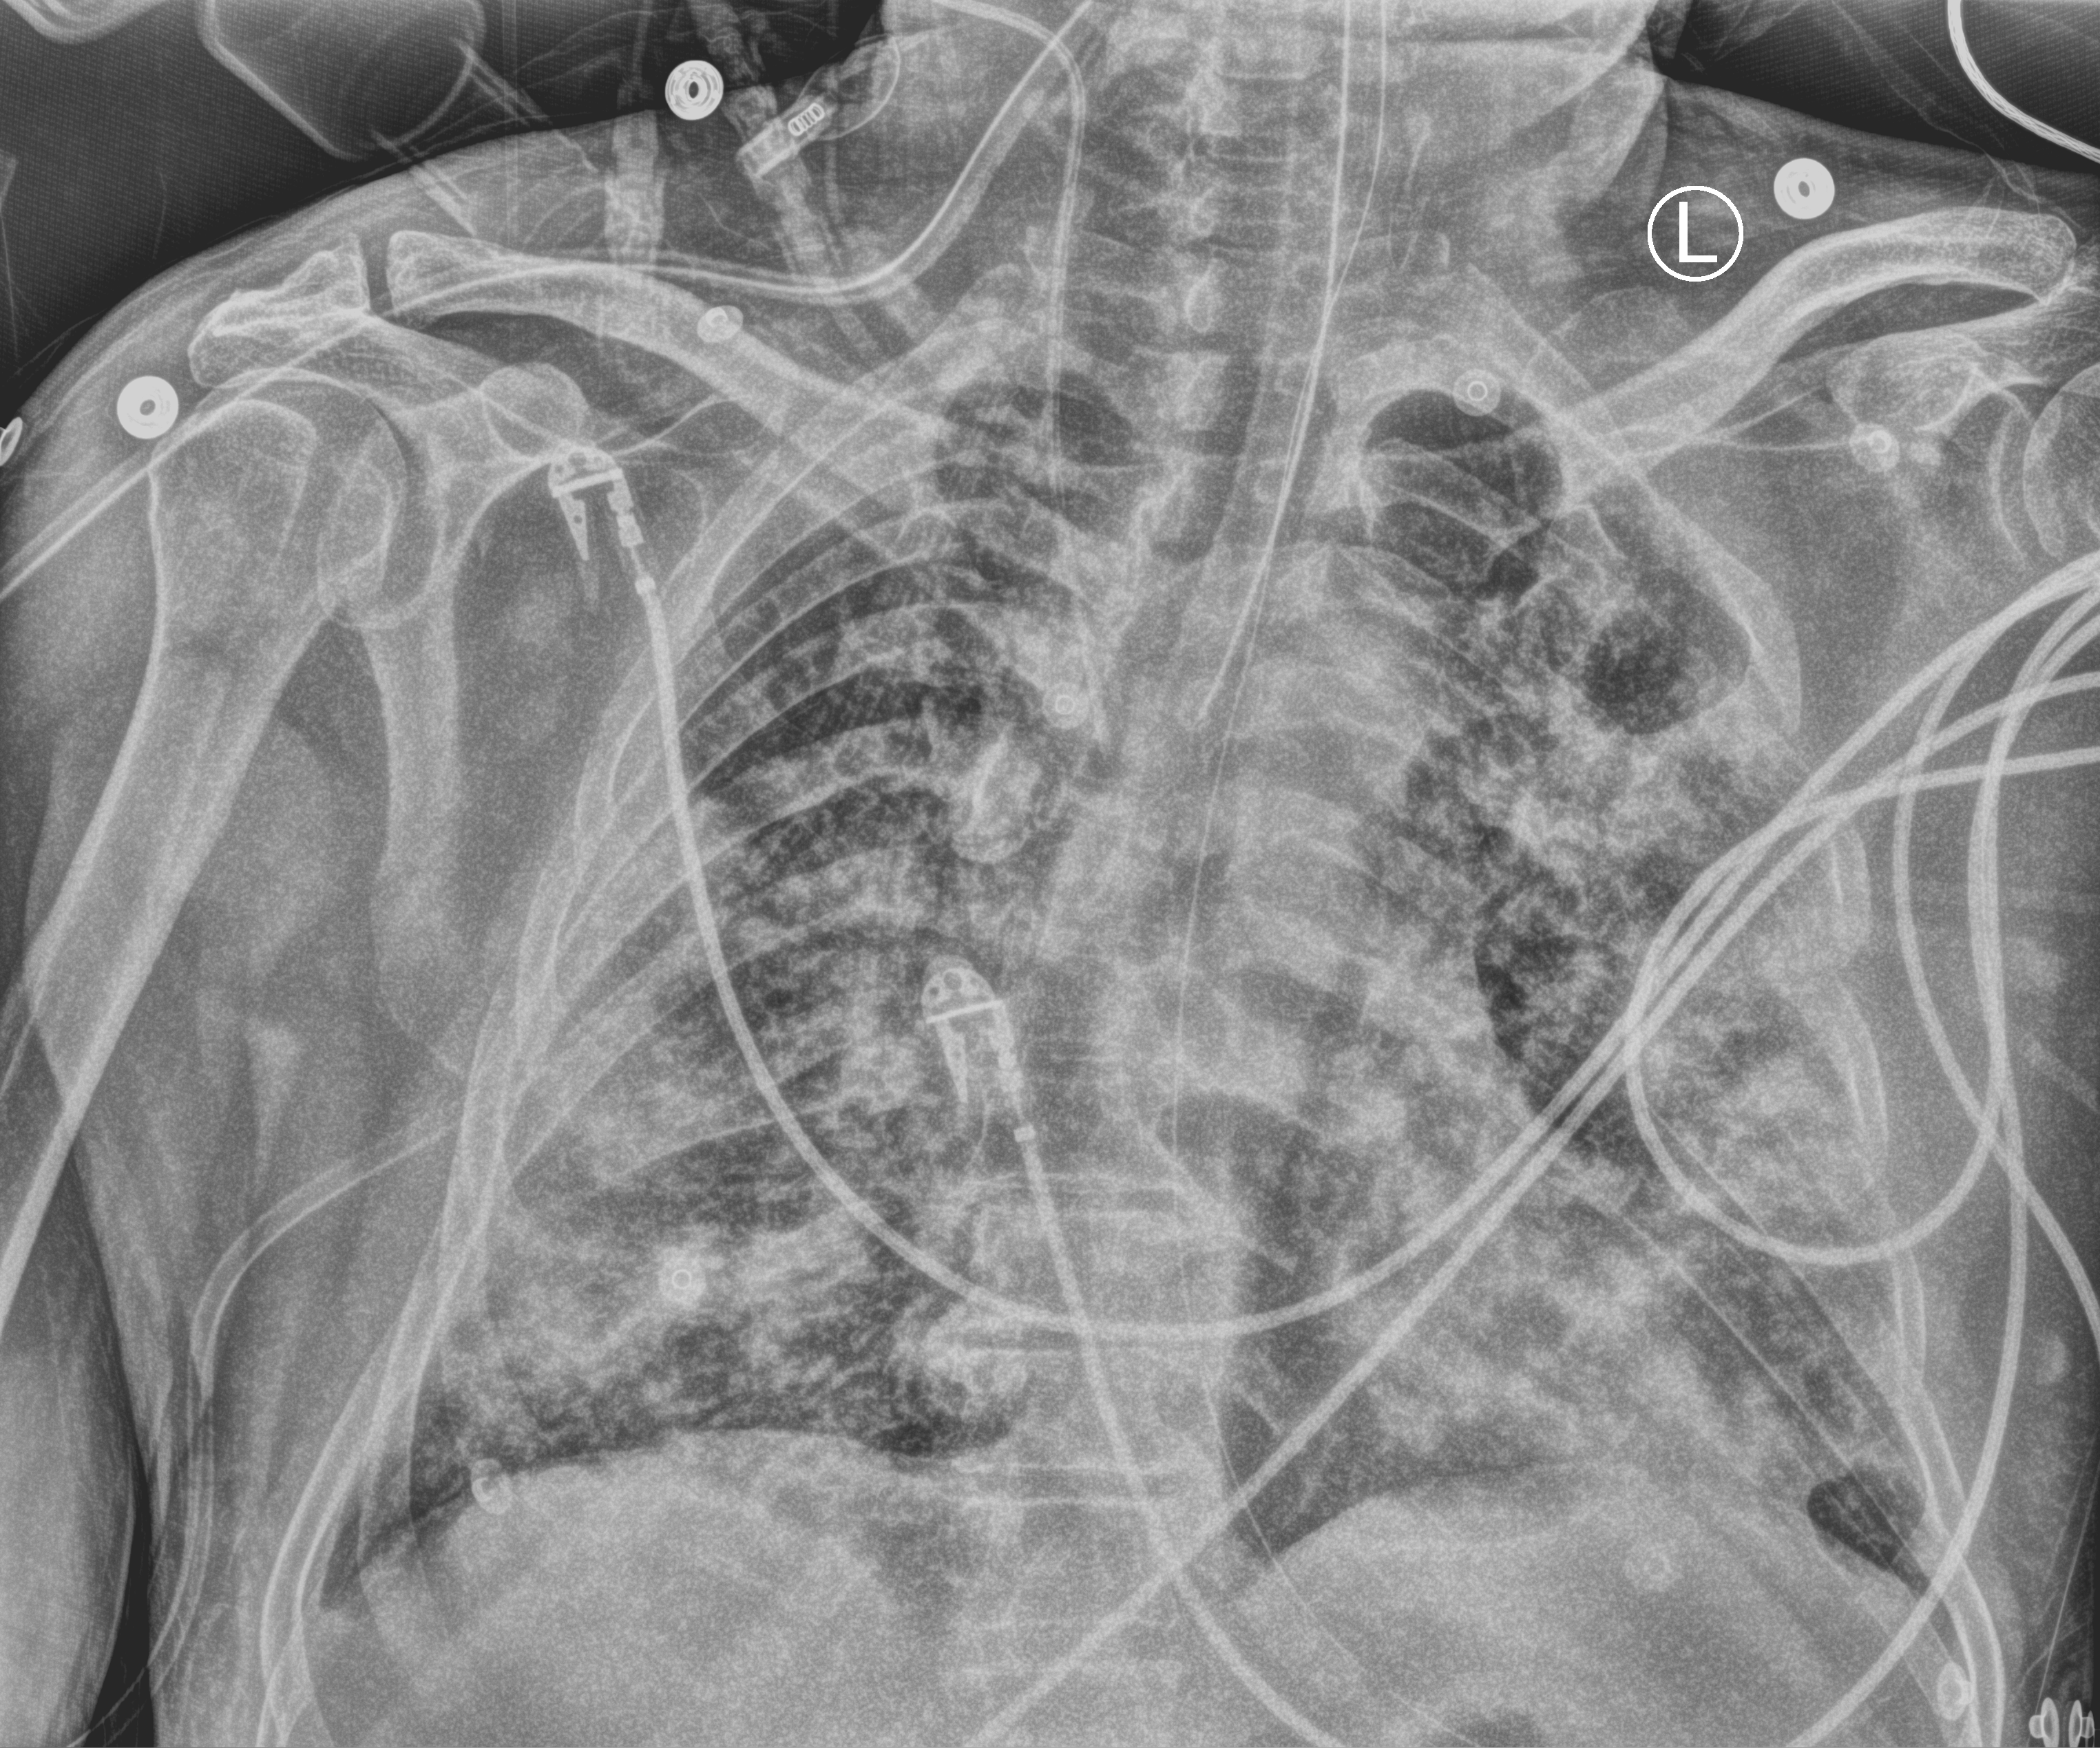
Chest X-ray (portable). Male patient hospitalised with COVID-19, age 60–74 years.
From the hospital-stay record, not from the radiograph (when in the stay this image was taken is not recorded):
- smoking status (admission record): never